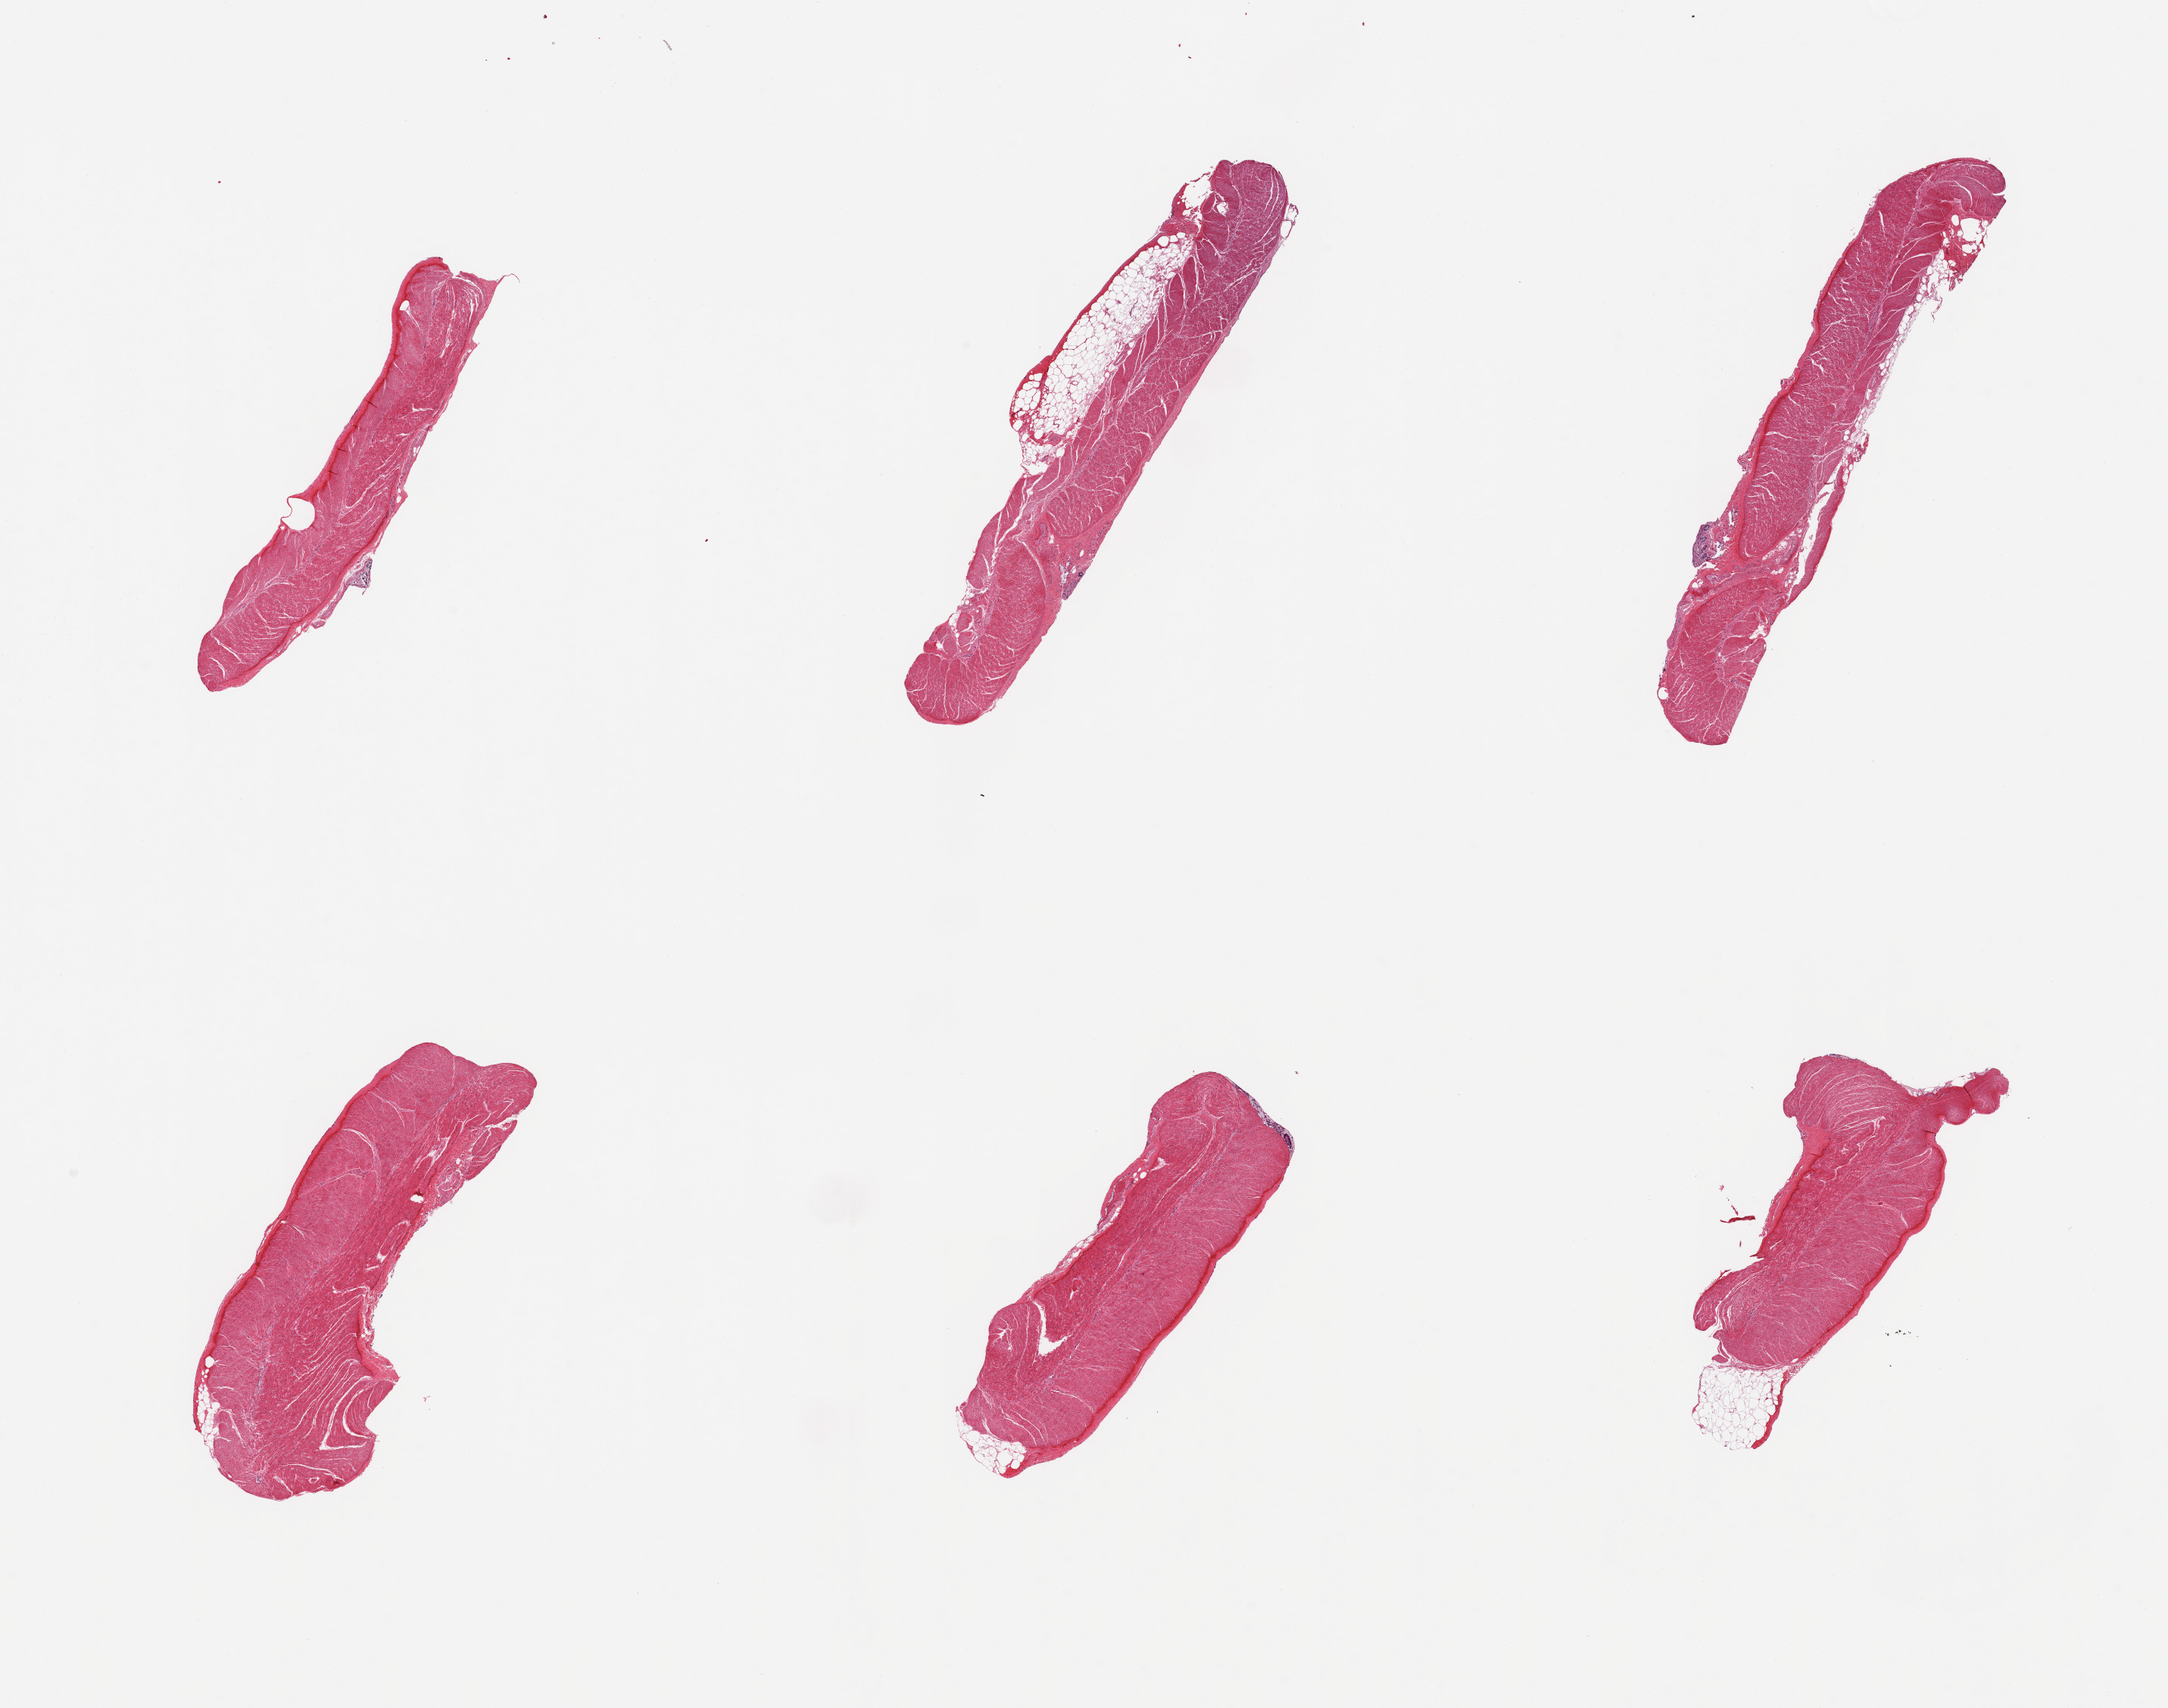
Digitized haematoxylin and eosin-stained section, whole scanned area (about 22.6 x 17.8 mm) shown as a low-resolution overview, PAXgene-fixed, paraffin-embedded tissue, target tissue: sigmoid colon, tissue donor sample. Donor: male.
- reviewer comment on this tissue sample: 6 pieces; mostly well dissected muscle; small foci of mucosa